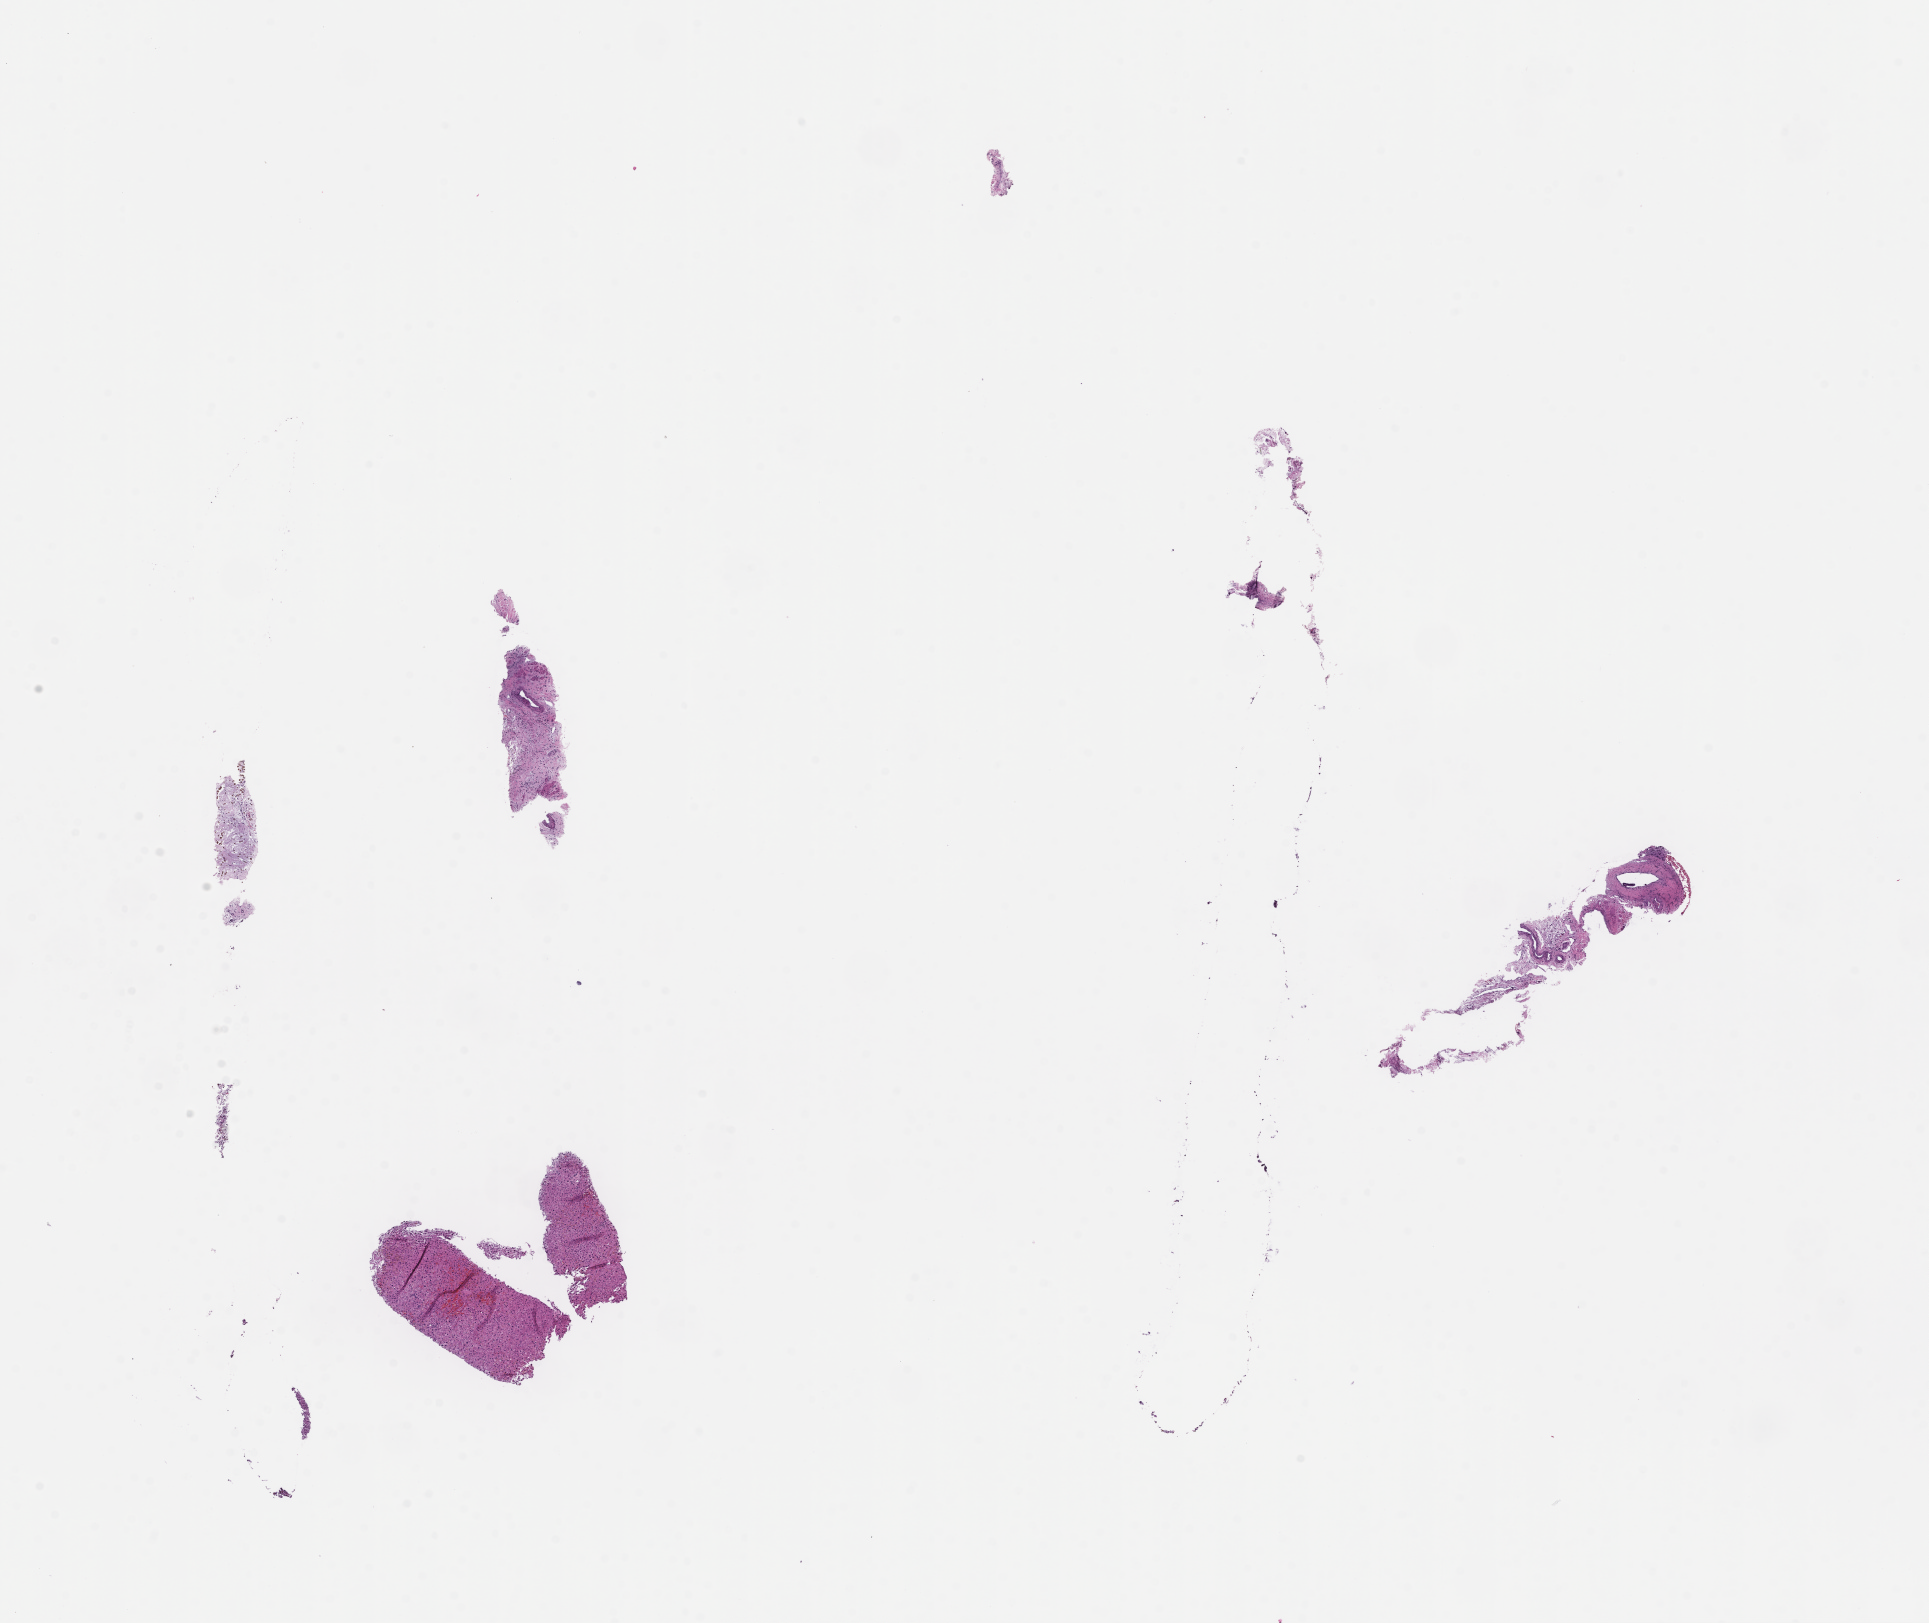
Digitized haematoxylin and eosin-stained section, a low-resolution overview of the entire scanned area, about 15.6 x 13.1 mm; FFPE section. Patient: female.
• this section: metastasis (sampled organ not recorded)
• patient diagnosis (primary): Invasive Breast Carcinoma